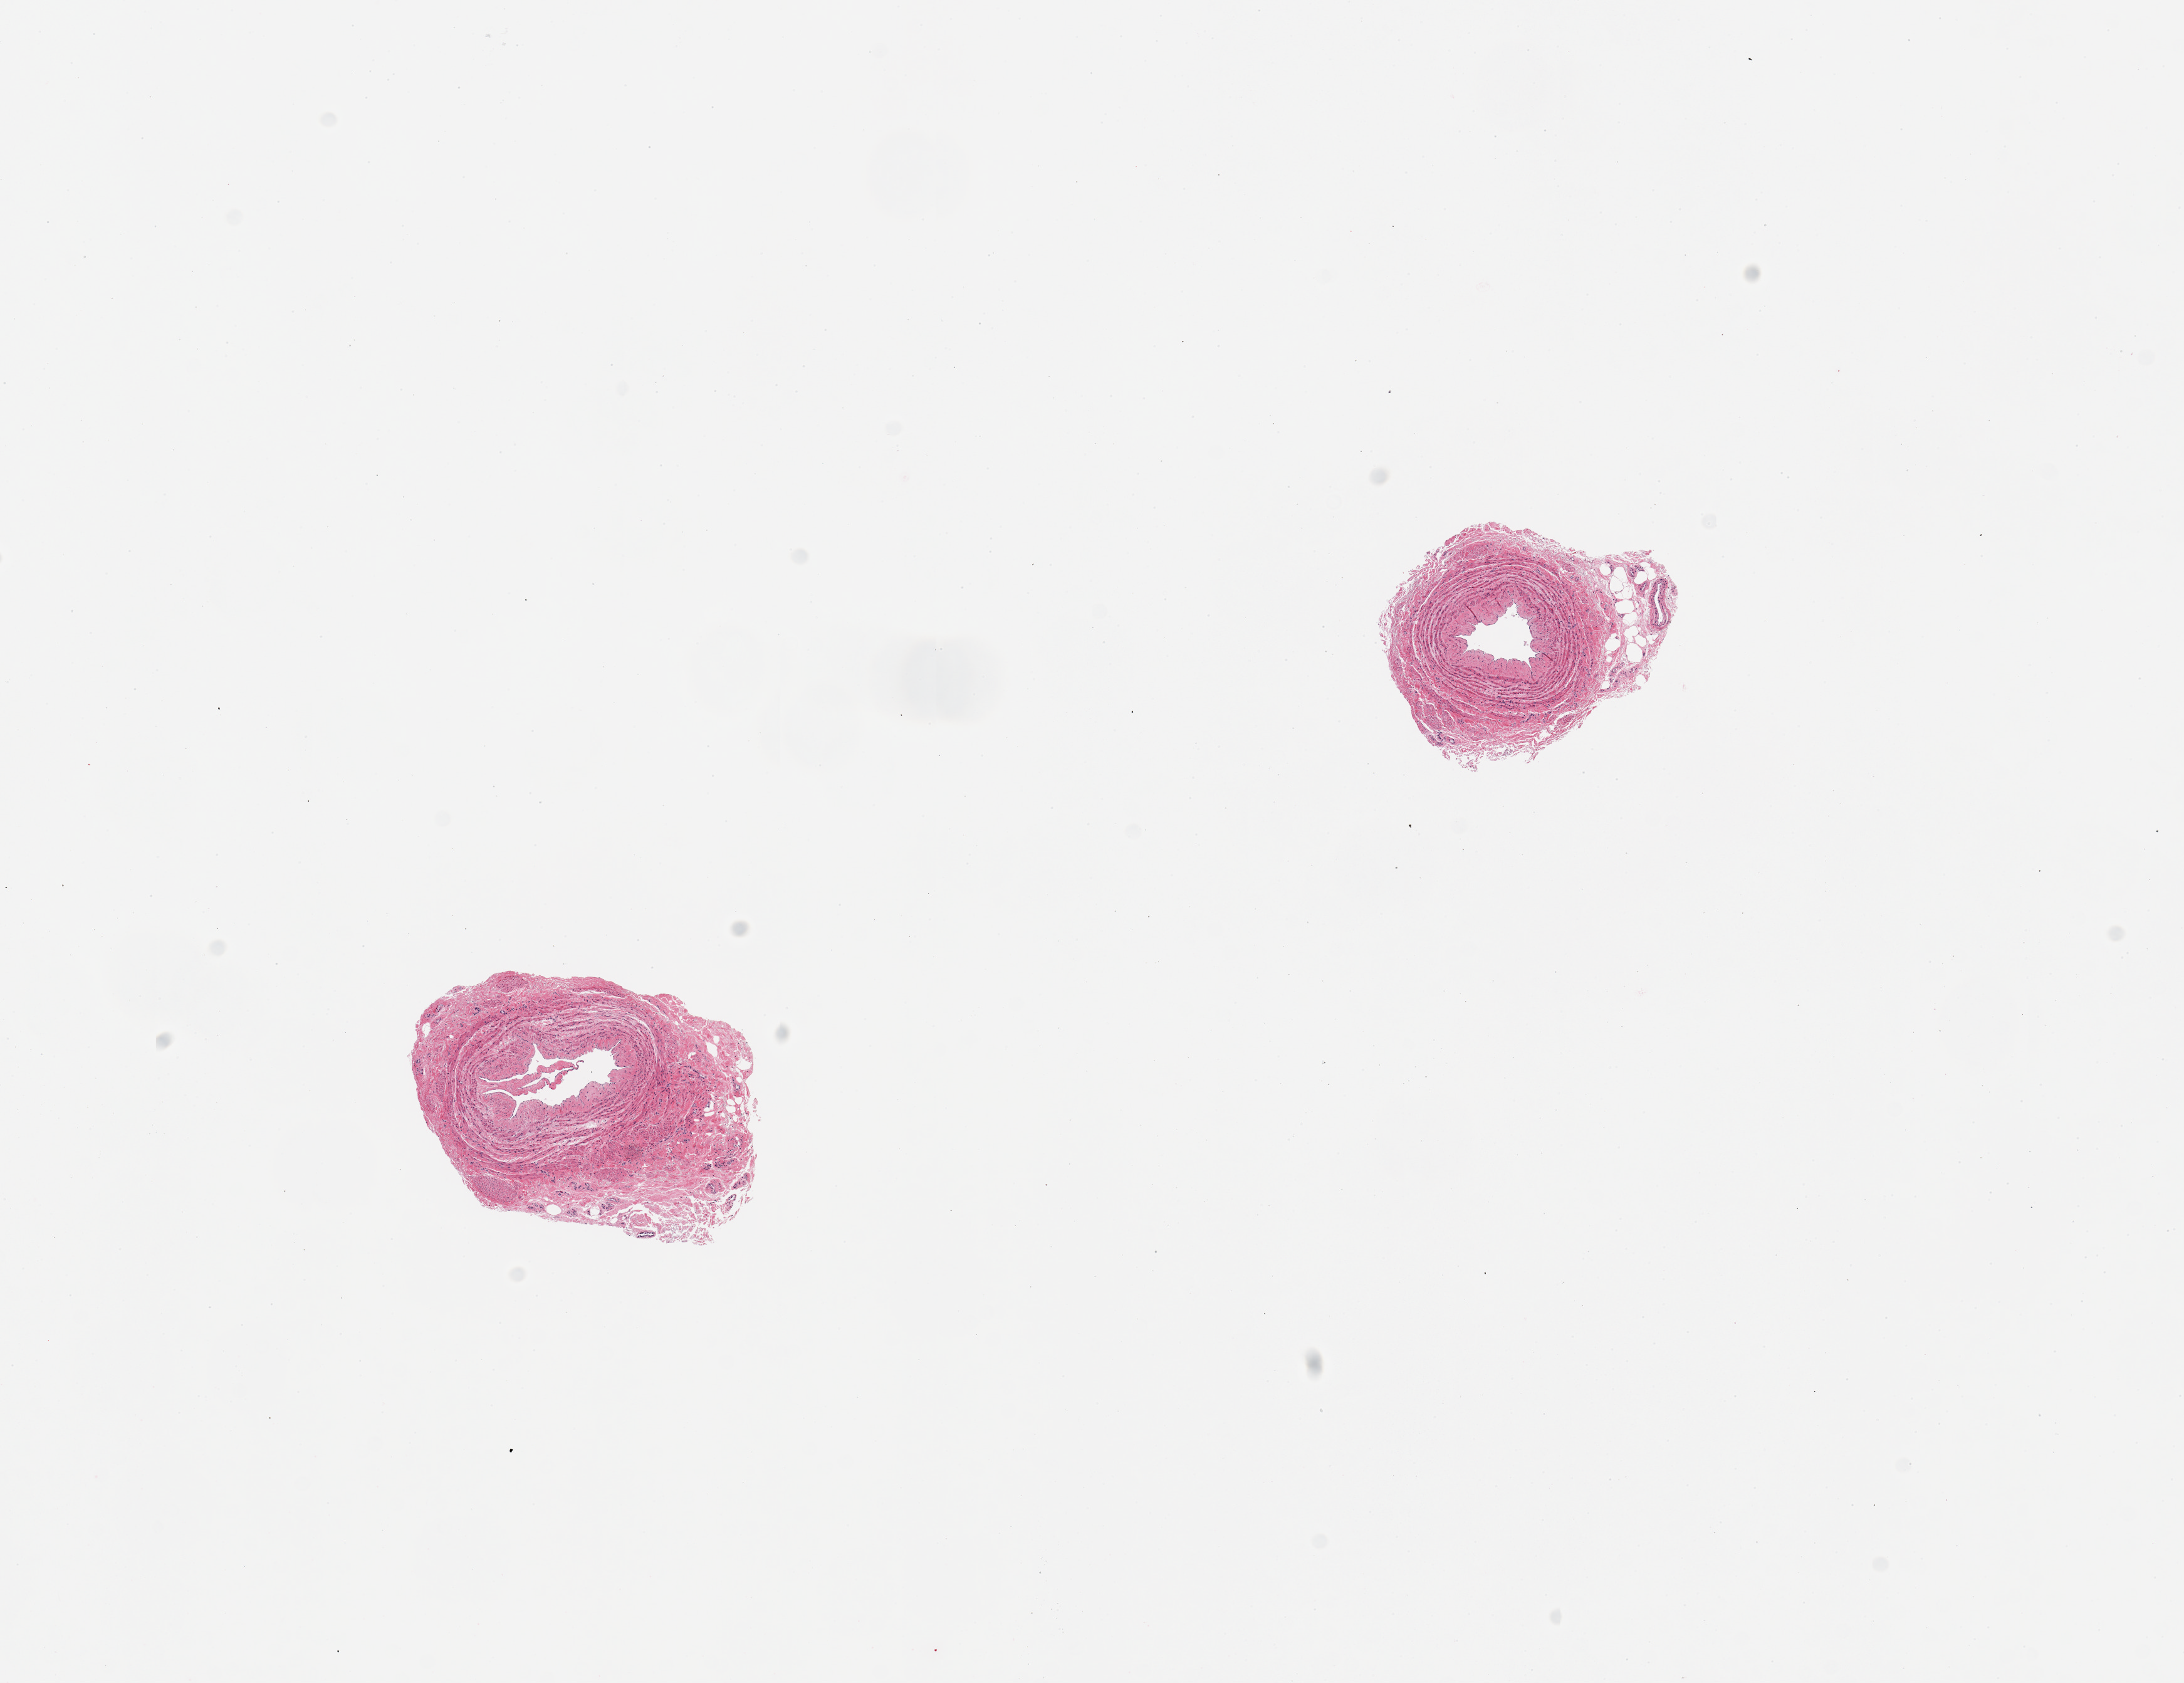
Digitized hematoxylin and eosin (H&E)-stained section, brightfield — a low-resolution overview of the entire scanned area, about 13.8 x 10.6 mm (from a 20x scan). PAXgene-fixed paraffin-embedded (PFPE) section. Sampled site (target tissue): tibial artery. Donor tissue sample. Female donor.
* reviewer comment on this tissue sample: 2 pieces; well trimmed